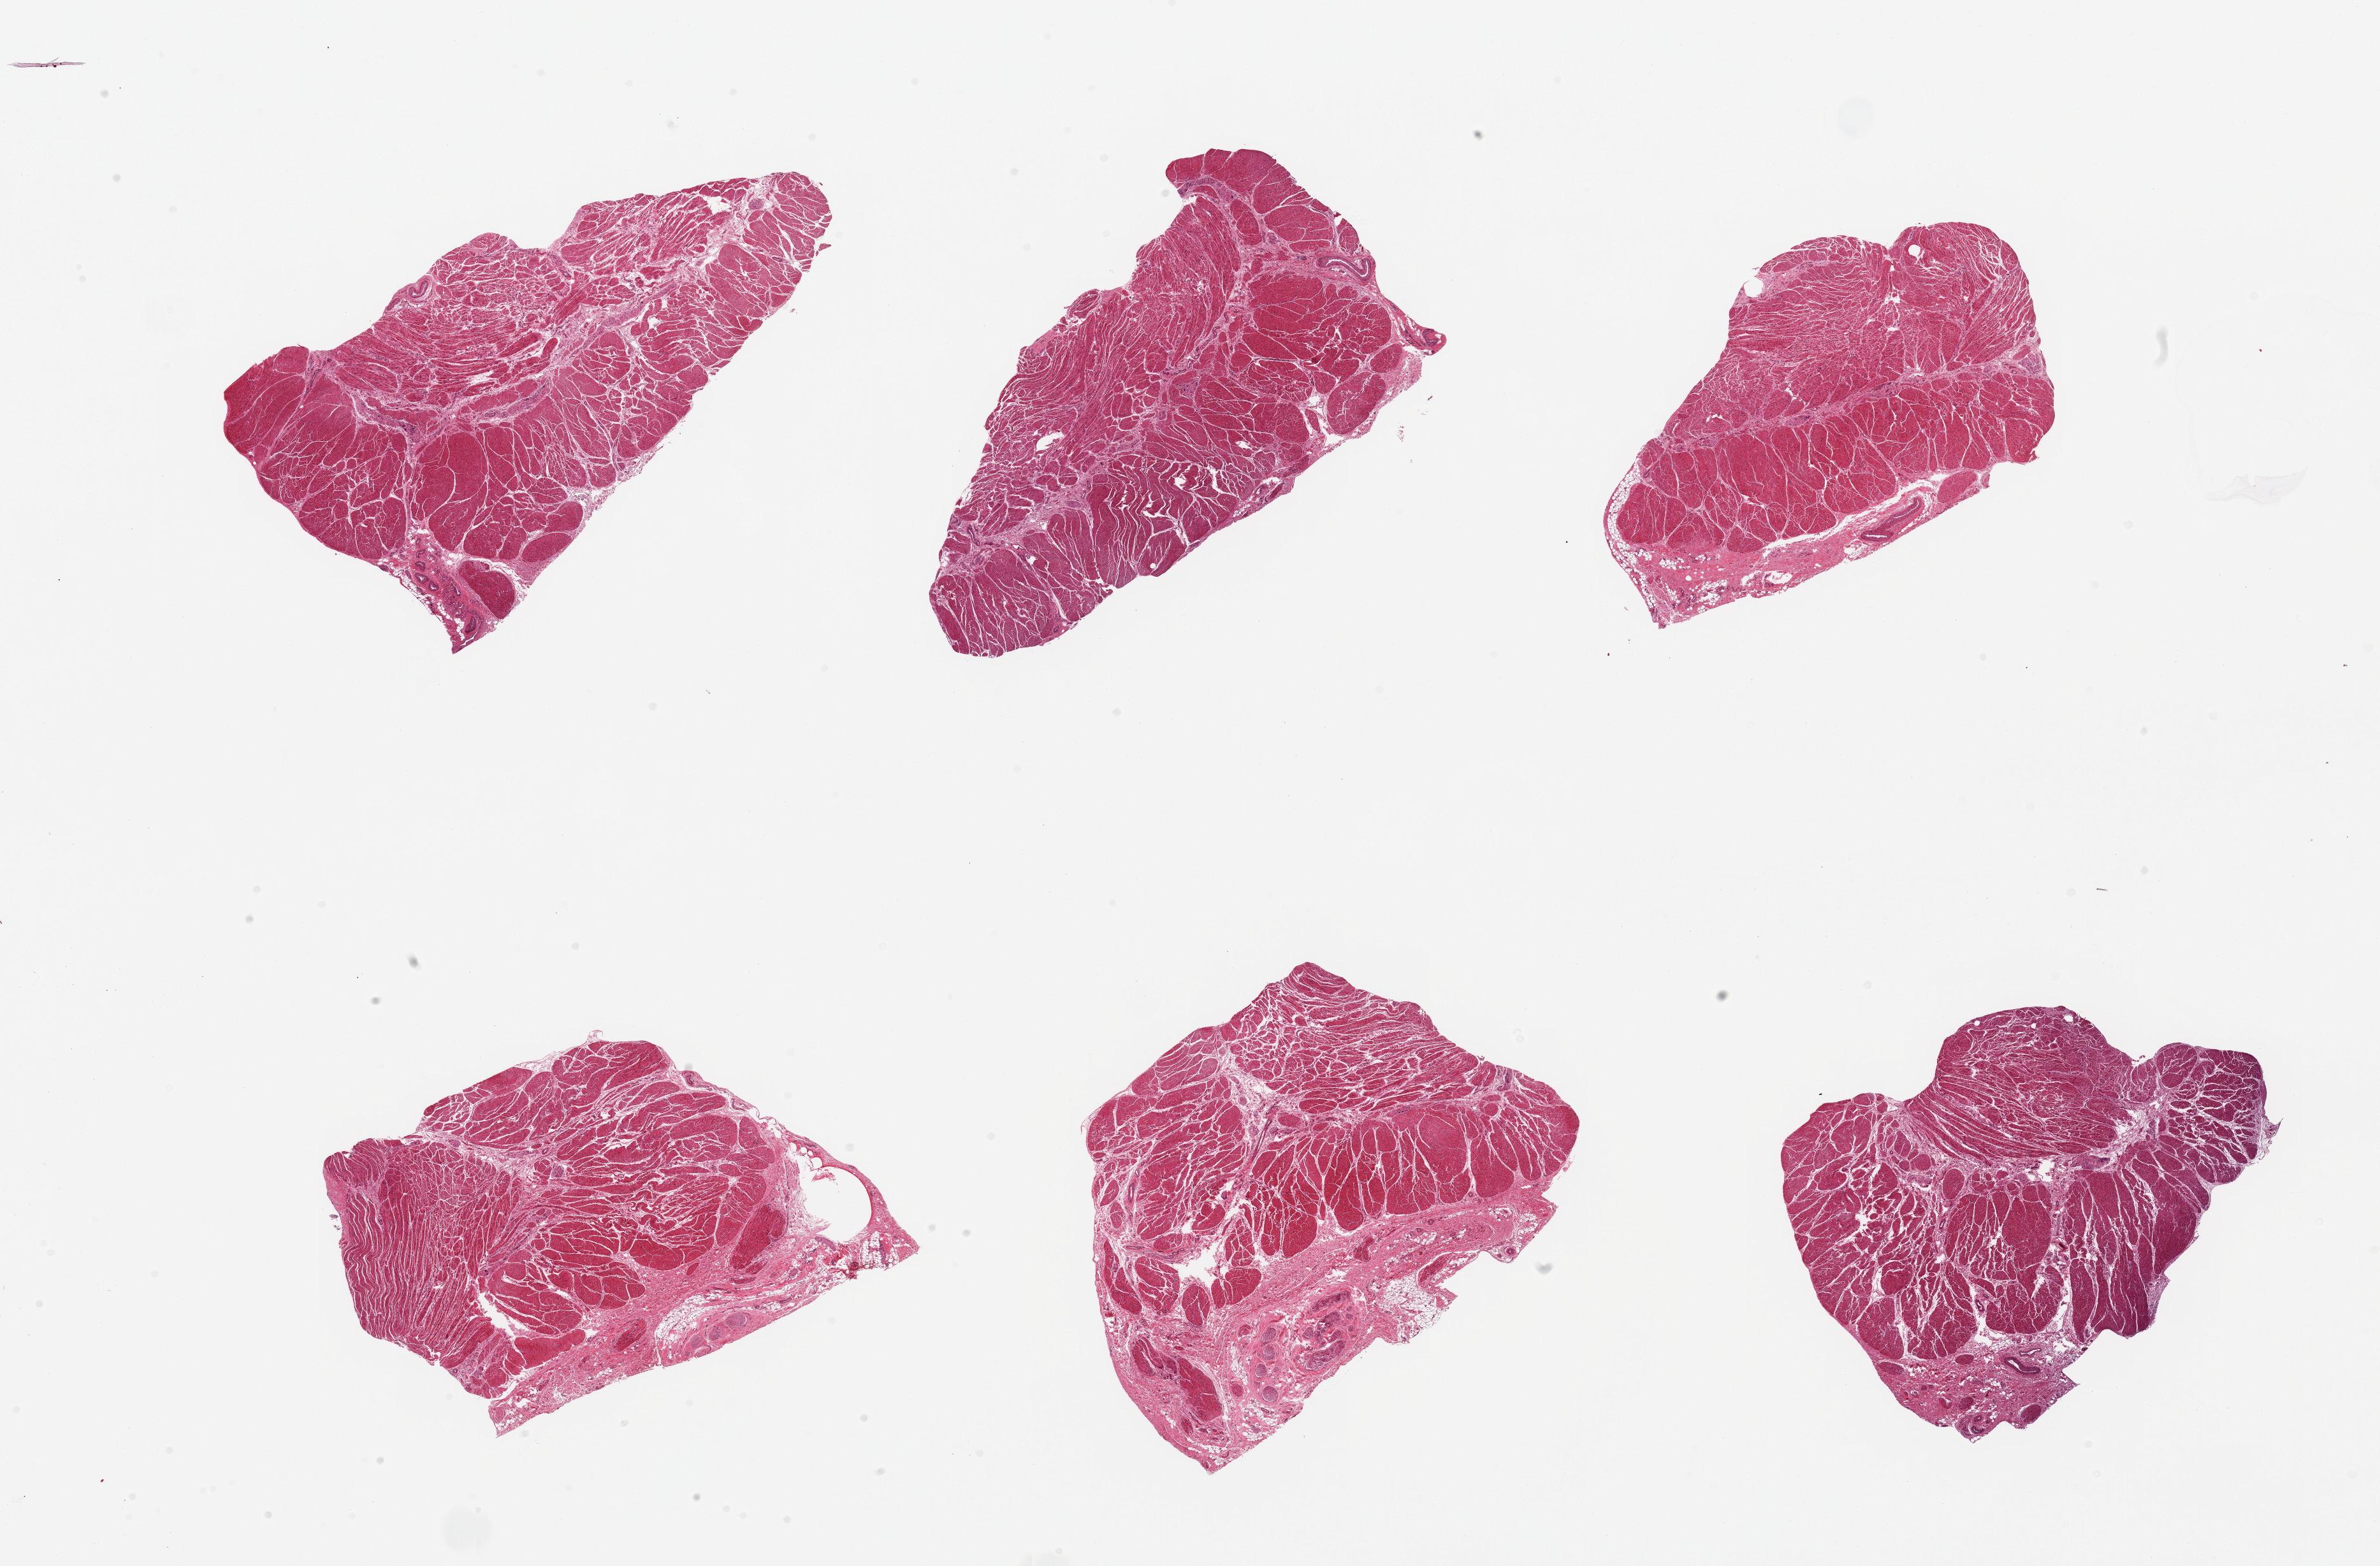
Digitized hematoxylin and eosin (H&E)-stained section, low-resolution overview of the scanned area, about 29.5 x 19.4 mm; PAXgene-fixed, paraffin-embedded tissue; section of esophageal muscle (target tissue); tissue donor sample. Donor: male.
Reviewer comment on this tissue sample: 6 pieces; submucosal stroma on 2 pieces.